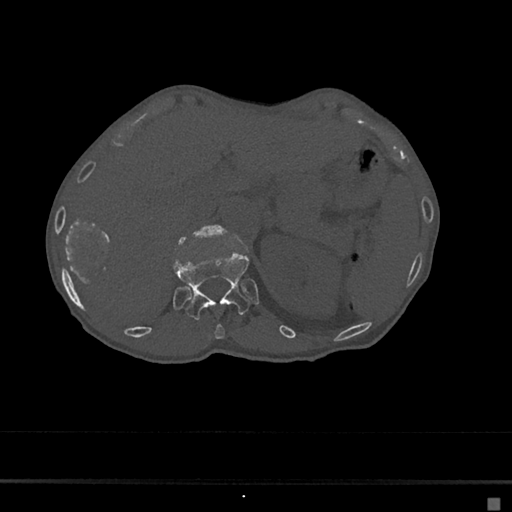
CT including the spine, one axial slice. Slice 125 of 797 in the series (ordered by position). Reconstruction kernel Br40s/3. Bone window (W 1800 / L 400 HU). 0.5 mm slice thickness. 512 × 512 image matrix. Patient: female, 68 years. From the clinical record (not read from this slice): primary cancer: renal.
Outlined on this slice (semi-automatic segmentation, software-assisted and operator-edited):
- L1 vertebra: bounding box [x1, y1, x2, y2] px = [179, 226, 224, 243]
- T11 vertebra: [214, 323, 225, 340]
- T12 vertebra: [173, 251, 250, 321]